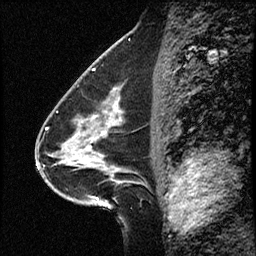
Breast MRI (dynamic contrast-enhanced), one sagittal slice. Dynamic contrast-enhanced study with each time point stored as its own series, time point 2 of 4 at this slice position (early post-contrast, ordered by acquisition time). 1.5 T. TE 4.2 ms, TR 17.5 ms. 3 mm slice thickness. 256 × 256 image matrix, field of view 200 × 200 mm. Case-level facts recorded for this patient, not image findings: setting: breast cancer imaged before/during neoadjuvant chemotherapy.
Outlined on this slice (semi-automatic segmentation, software-assisted and operator-edited):
- analysis volume of interest (the breast-tissue region the enhancement analysis was run in; not a lesion): bounding box (x1, y1, x2, y2) in pixels: (52, 98, 158, 207)
- tumour enhancement mask (voxels above the 100 % enhancement threshold inside the analysis volume of interest): (81, 99, 120, 162)